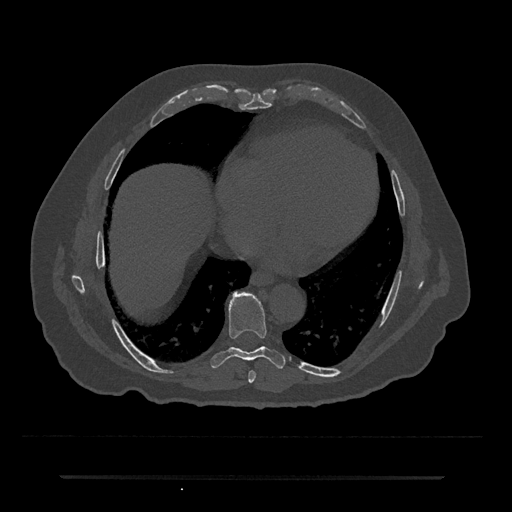
CT including the spine, one axial slice; slice 333 of 797 in the series (ordered by position); 120 kVp; bone window (W 1800 / L 400 HU); 0.5 mm slice thickness; 512 × 512 image matrix, field of view 437 × 437 mm. Patient: male, 69 years. Case-level facts recorded for this patient, not image findings: primary cancer: prostate.
Structures marked on this image (semi-automatic segmentation, software-assisted and operator-edited):
- T7 vertebra: bounding box (x1, y1, x2, y2) in pixels: (248, 371, 256, 383)
- T8 vertebra: (211, 292, 285, 369)